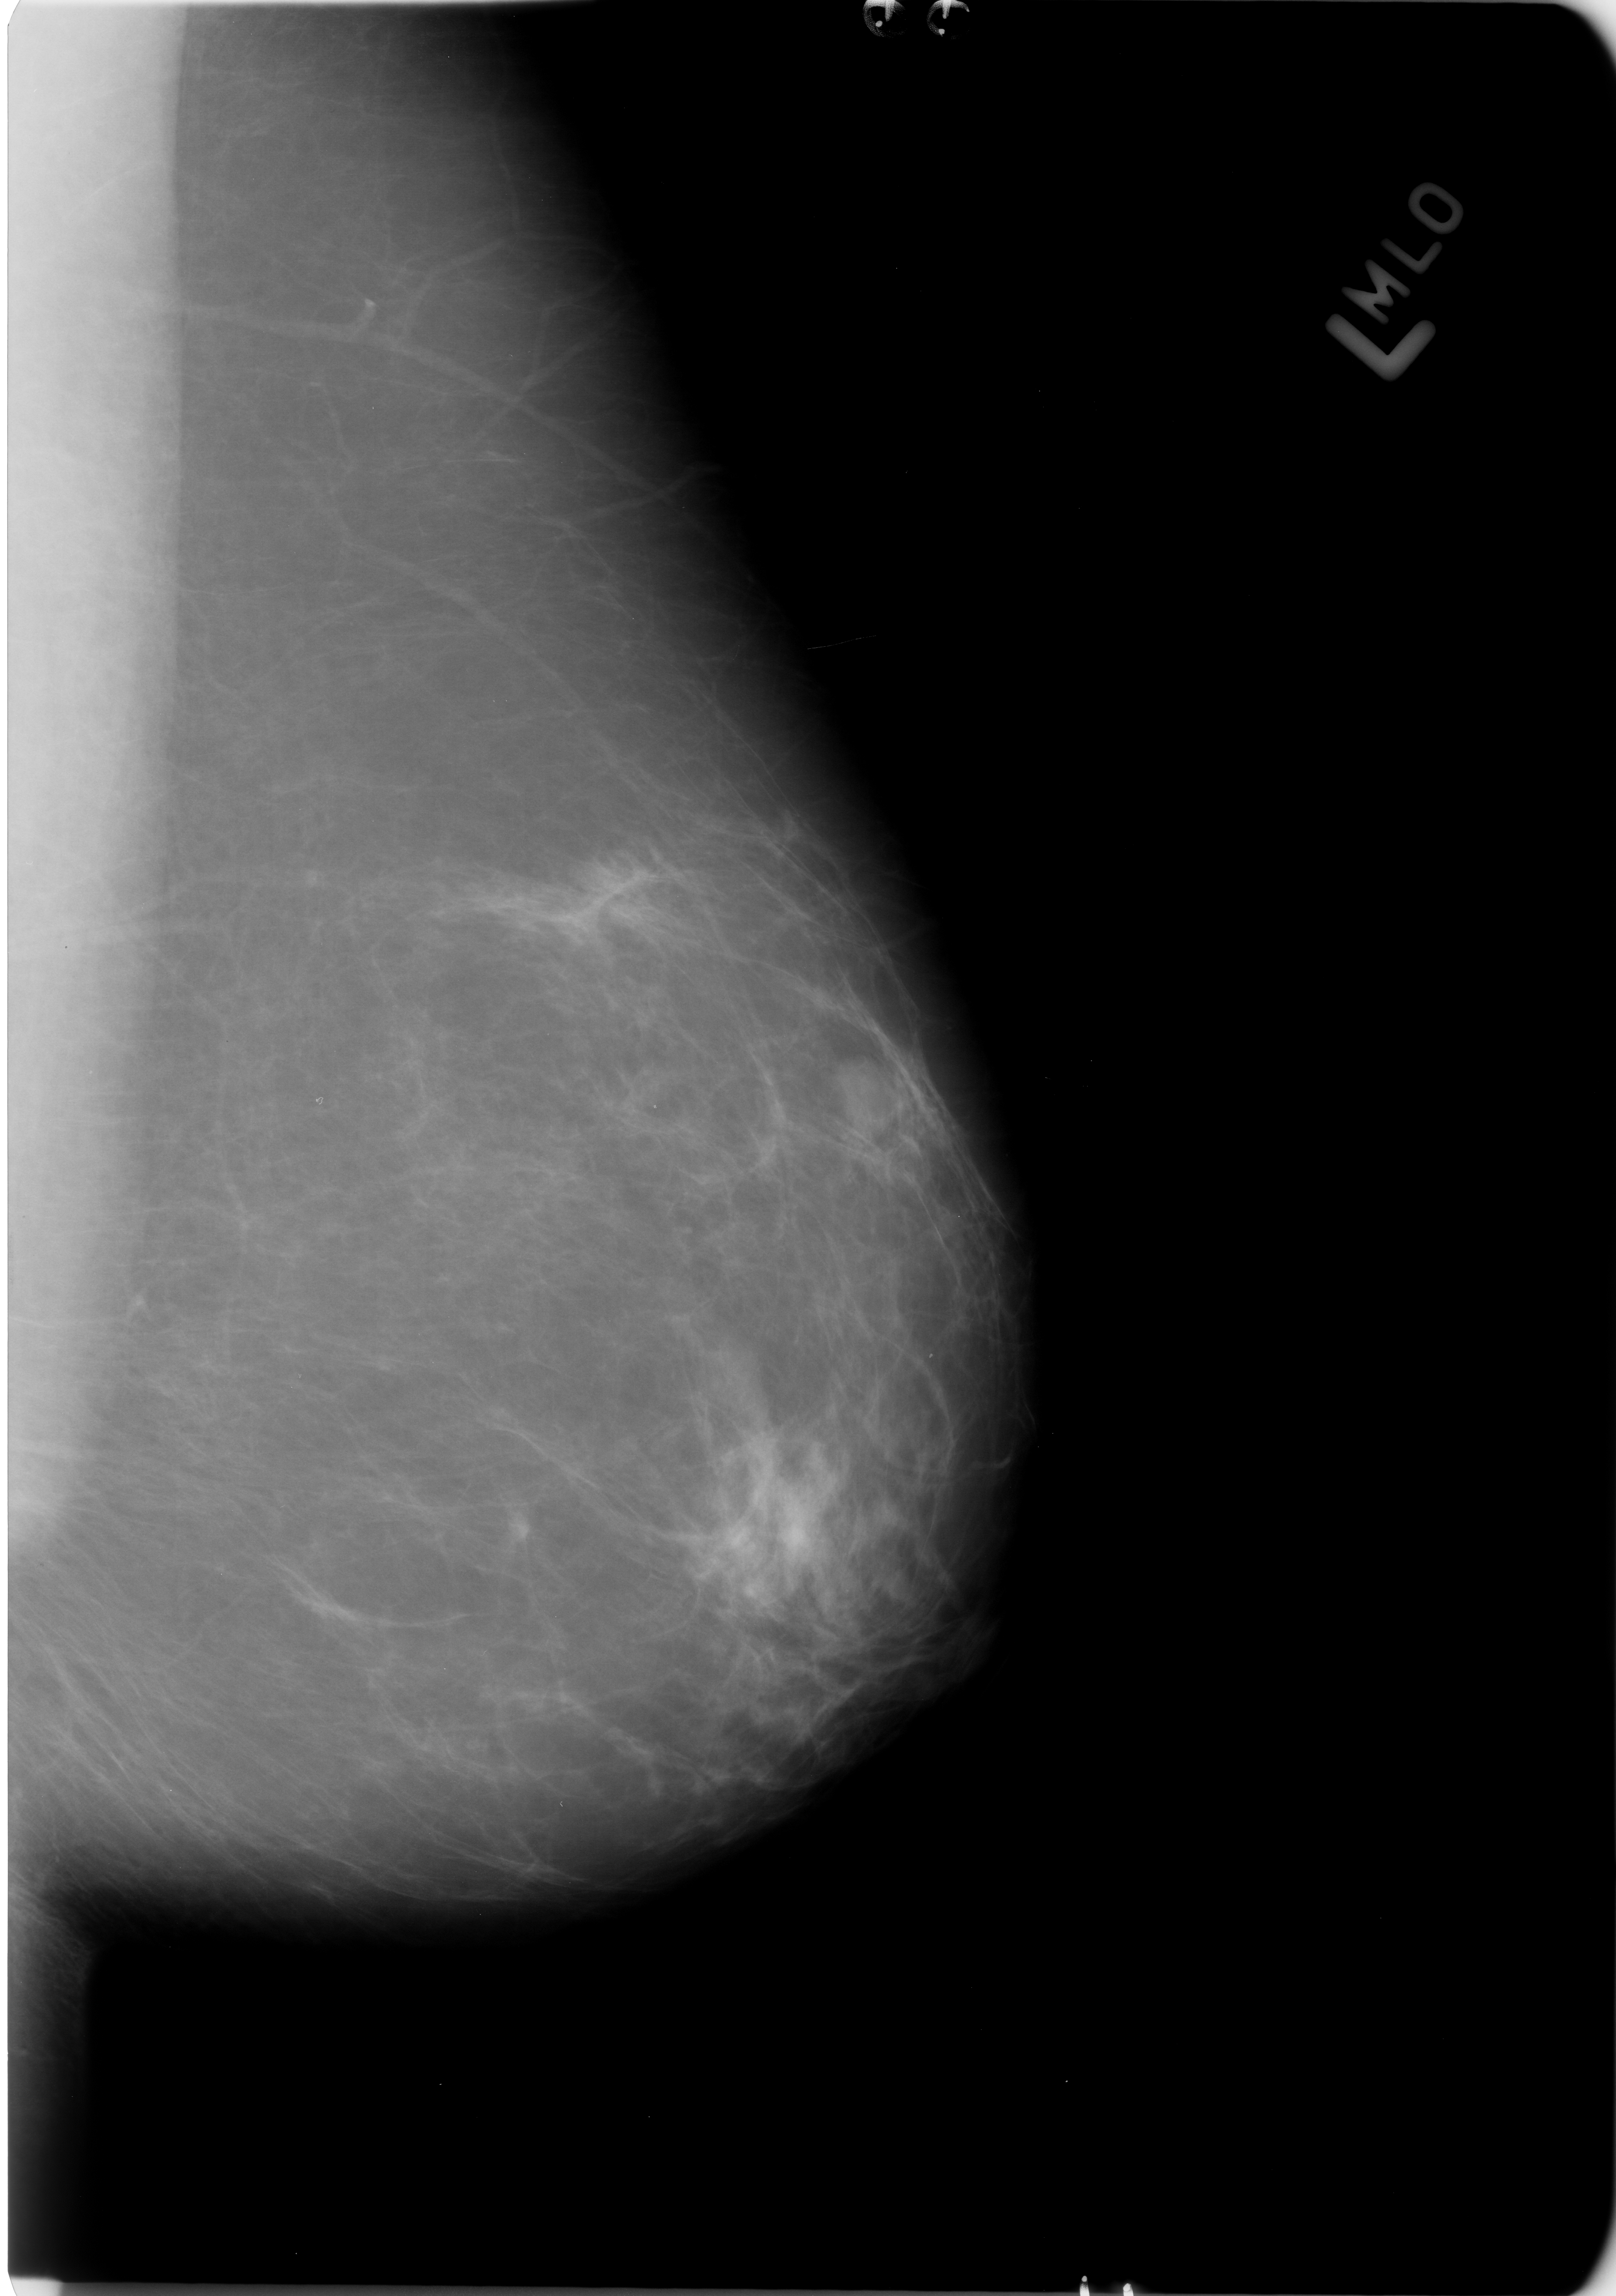
Mammogram (digitized film), left breast, MLO view, breast composition: scattered fibroglandular densities (BI-RADS density category 2 of 4).
Finding: mass, shape lobulated, margins circumscribed; BI-RADS assessment category 3; pathology (as recorded): benign.